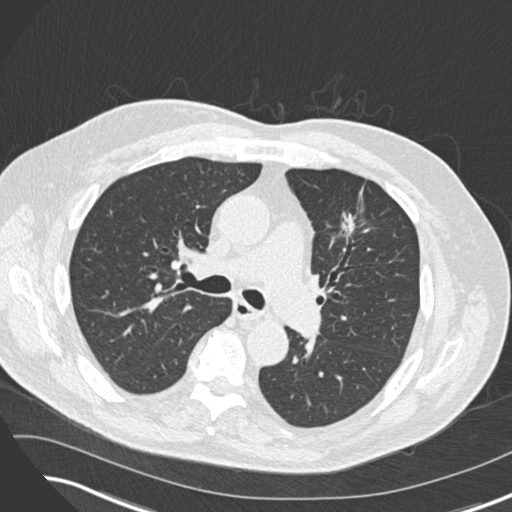
Low-dose screening chest CT, one axial slice; slice 103 of 169 in the series (ordered by position); reconstruction kernel B30f; 120 kVp; lung window (W 1500 / L -600 HU); 2 mm slice thickness; 512 × 512 image matrix.
Annotated regions visible in this slice (manually delineated by an expert):
- lesion 1 (tumor, upper lobe of left lung): bounding box <342,213,354,240> (left, top, right, bottom; pixels)